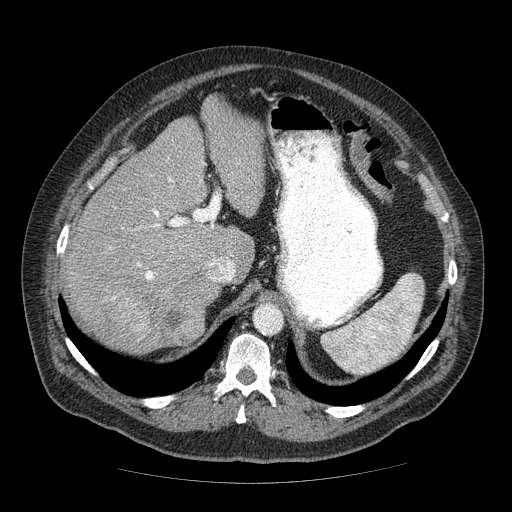
Contrast-enhanced abdominal CT (liver protocol), one axial slice; slice 43 of 85 in the series (ordered by position); reconstruction kernel STANDARD; soft-tissue window (W 400 / L 40 HU); 2.5 mm slice thickness; 512 × 512 image matrix, field of view 420 × 420 mm. From the clinical record (not read from this slice): diagnosis: hepatocellular carcinoma (patient treated with transarterial chemoembolisation; whether this scan precedes or follows treatment is not stated here); TNM stage (as recorded): Stage-IIIA; Child-Pugh class: A; tumour nodularity: multinodular; tumour size: 7 cm.
Outlined on this slice (semi-automatically segmented with operator editing):
- liver parenchyma outside the tumour (the mass and vessels are separate outlines, so this box may not span the whole liver): bounding box <64,98,264,350> (left, top, right, bottom; pixels)
- mass: <106,274,216,355>
- liver vessels: <110,177,213,300>